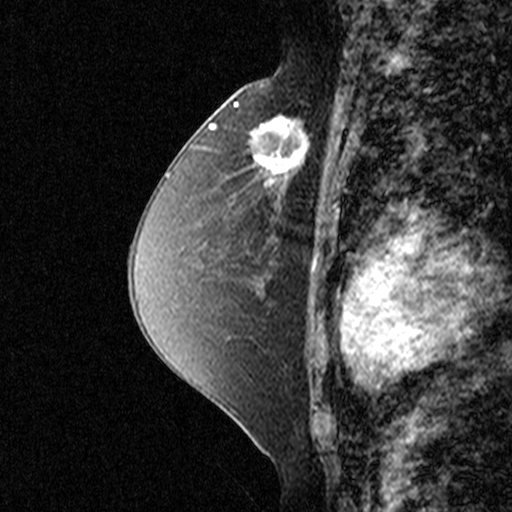
Breast MRI (dynamic contrast-enhanced), one sagittal slice; slice 25 of 44 in the series (ordered by position); dynamic contrast-enhanced study with each time point stored as its own series, time point 2 of 3 at this slice position (early post-contrast, ordered by acquisition time); 1.5 T; TE 4.5 ms, TR 11 ms; 3 mm slice thickness; 512 × 512 image matrix, field of view 200 × 200 mm. Female patient, age 49 years. Case-level facts recorded for this patient, not image findings: setting: breast cancer imaged before/during neoadjuvant chemotherapy; receptor status: triple-negative.
Annotated regions visible in this slice (semi-automatic segmentation, software-assisted and operator-edited):
- analysis volume of interest (the breast-tissue region the enhancement analysis was run in; not a lesion): box from (x=244, y=100) to (x=335, y=197) px
- tumour enhancement mask (voxels above the 90 % enhancement threshold inside the analysis volume of interest): (x=255, y=114)–(x=308, y=191)